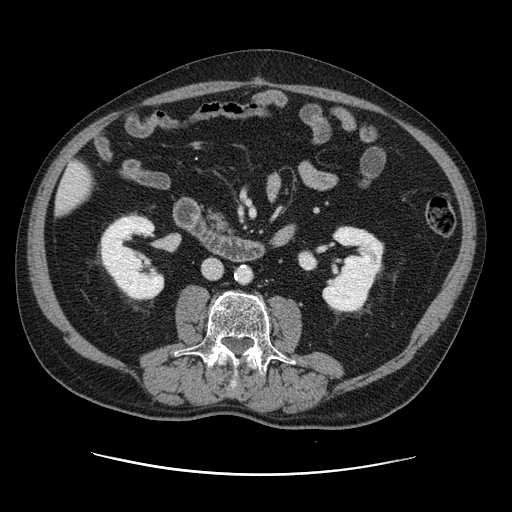
Contrast-enhanced abdominal CT, one axial slice; position 31 of 141 along the scan axis; 120 kVp; intravenous contrast given; soft-tissue window (W 400 / L 40 HU); 2.5 mm slice thickness; 512 × 512 image matrix. Male patient, age 72 years. Case-level facts recorded for this patient, not image findings: diagnosis: colorectal cancer liver metastases, imaged before liver resection; multiple liver metastases: yes; largest metastasis: 5.4 cm; chemotherapy before resection: yes.
Annotated regions visible in this slice (manually delineated by an expert):
- liver: box from (x=58, y=163) to (x=93, y=212) px
- planned liver remnant (the part of the liver to remain after resection): (x=58, y=163)–(x=92, y=212)